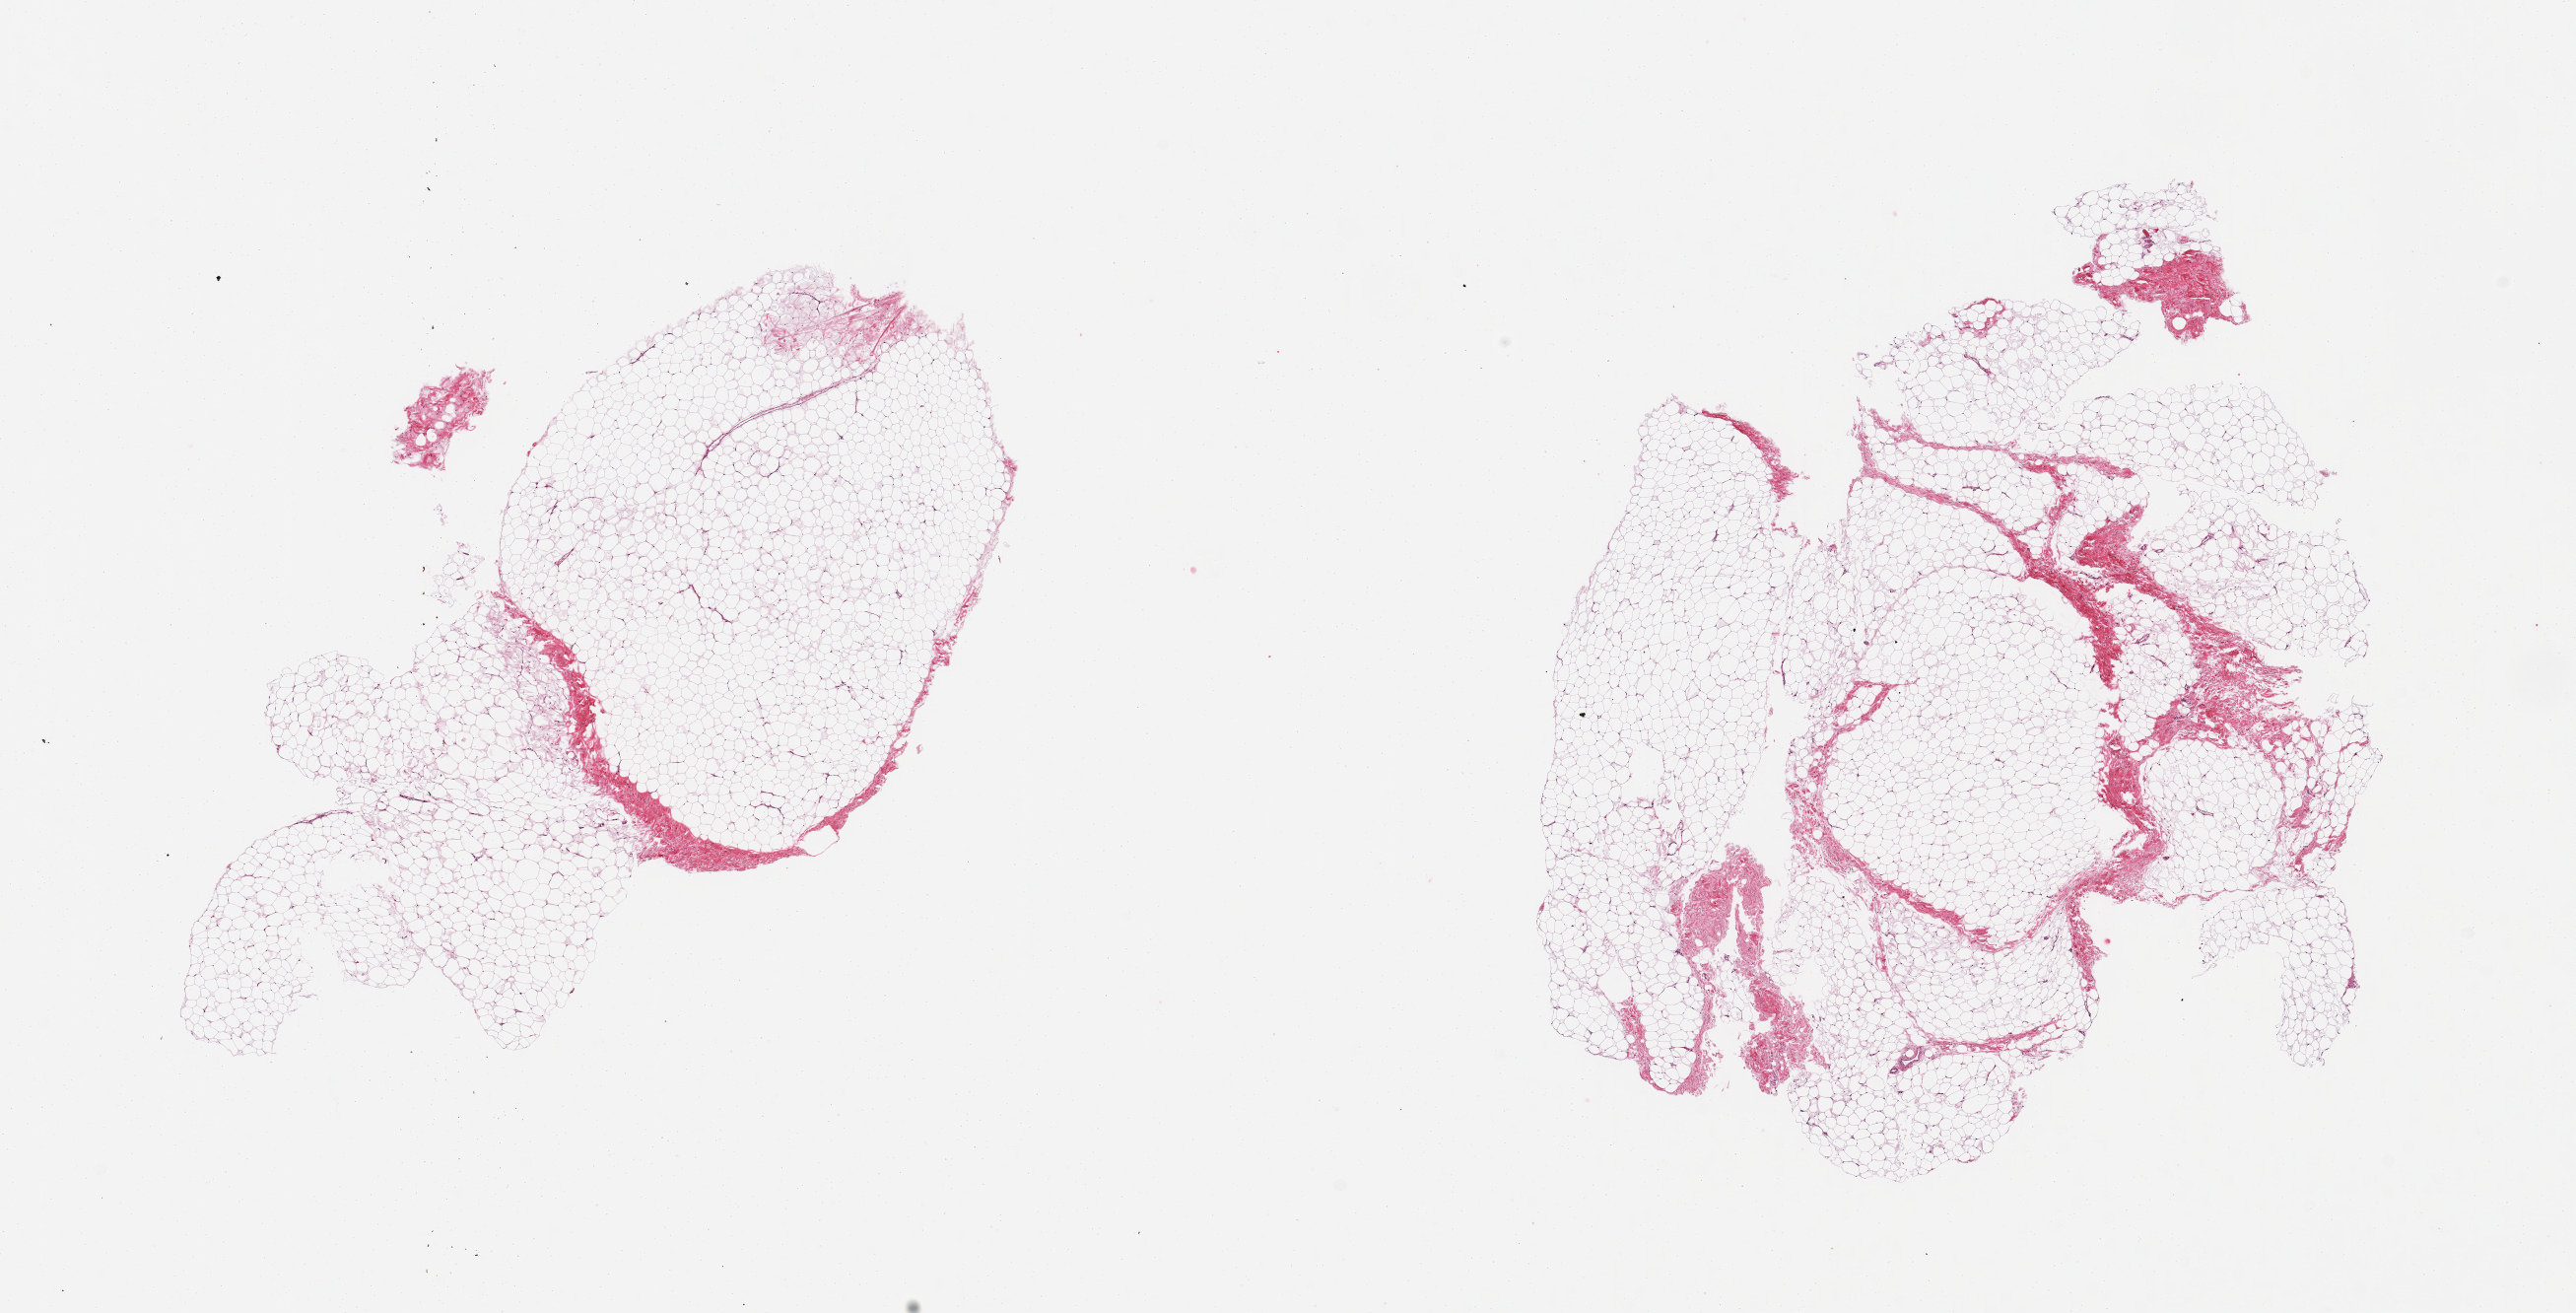
Digitized hematoxylin and eosin (H&E)-stained section, brightfield, a low-resolution overview of the entire scanned area, about 20.7 x 10.5 mm (slide scanned at 20x); PAXgene-fixed paraffin-embedded (PFPE) section; target tissue: breast; donor tissue sample. Donor: male.
* review note (as recorded): 2 pieces, fibroadipose elements only